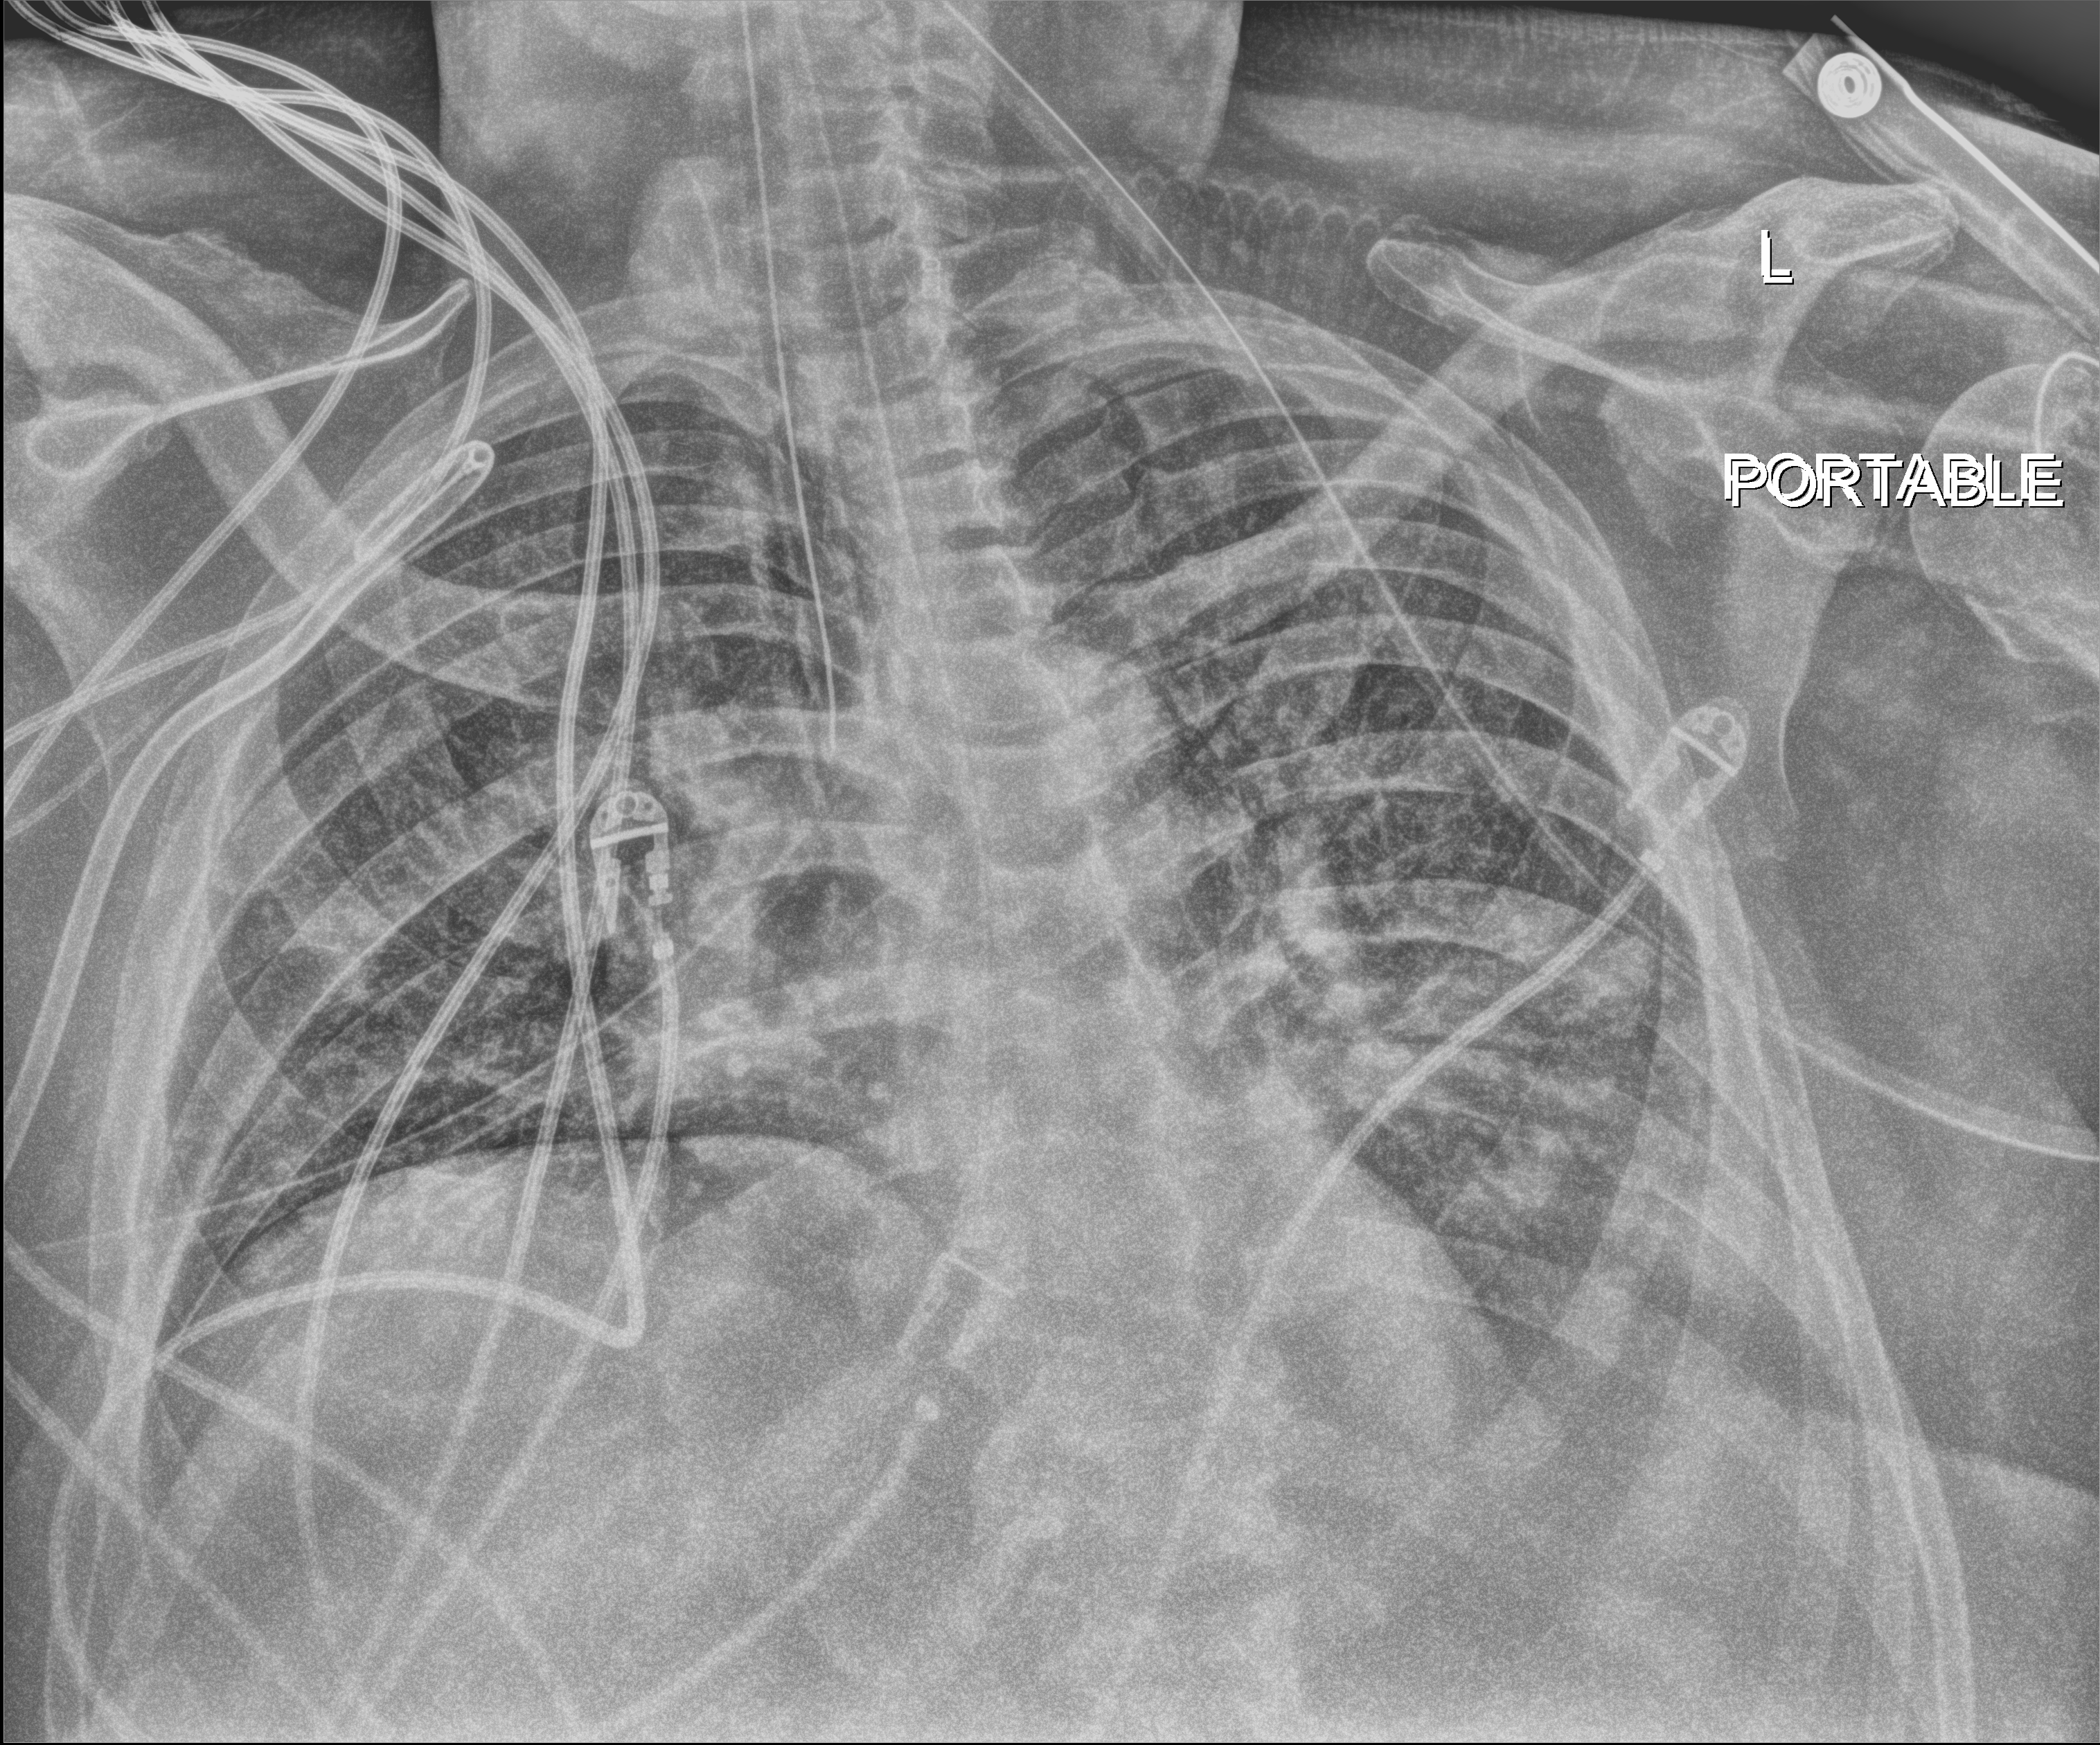
Portable chest radiograph; anteroposterior (AP) projection. Patient hospitalised with COVID-19; male, aged 60–74 years.
Hospital-stay facts (about this admission, not read from this image; timing relative to this image not recorded):
- mechanically ventilated during this hospital stay: yes